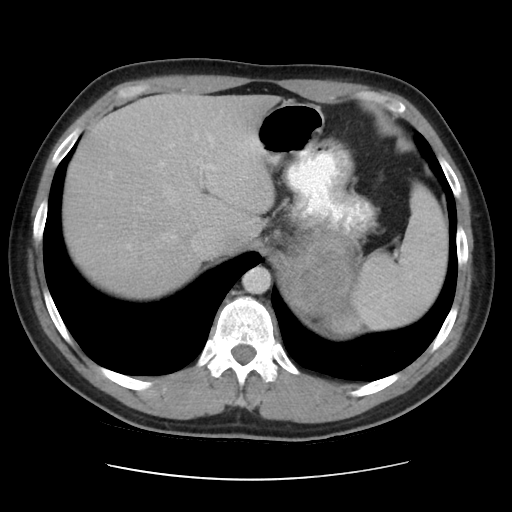
Contrast-enhanced abdominal CT, one axial slice; reconstruction kernel STANDARD; intravenous contrast given; soft-tissue window (W 400 / L 40 HU); 5 mm slice thickness; 512 × 512 image matrix, field of view 360 × 360 mm. Patient: male, 32 years. From the clinical record (not read from this slice): diagnosis: adrenocortical carcinoma; tumour side: left adrenal; tumour size at pathology: 14 cm; Ki-67 index: 67 %; stage (as recorded): 3.
Outlined on this slice (semi-automatic segmentation, software-assisted and operator-edited):
- mass: bounding box [x1, y1, x2, y2] px = [291, 235, 357, 331]